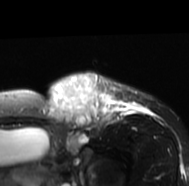
MRI of an extremity soft-tissue mass, one axial slice; position 55 of 77 along the scan axis; T2-weighted fat-saturated; MR volume resampled by the dataset authors to the PET/CT grid (not the native acquisition matrix); 3.27 mm slice thickness; 189 × 186 image matrix, field of view 185 × 182 mm. Female patient. From the clinical record (not read from this slice): histological type: leiomyosarcoma; grade: high; site of the primary tumour: groin.
Outlined on this slice (expert contour drawn on MRI and transferred to this co-registered scan by the dataset authors):
- gross tumour volume including surrounding oedema: bounding box [x1, y1, x2, y2] px = [45, 72, 153, 137]
- gross tumour volume (mass): [47, 72, 105, 128]